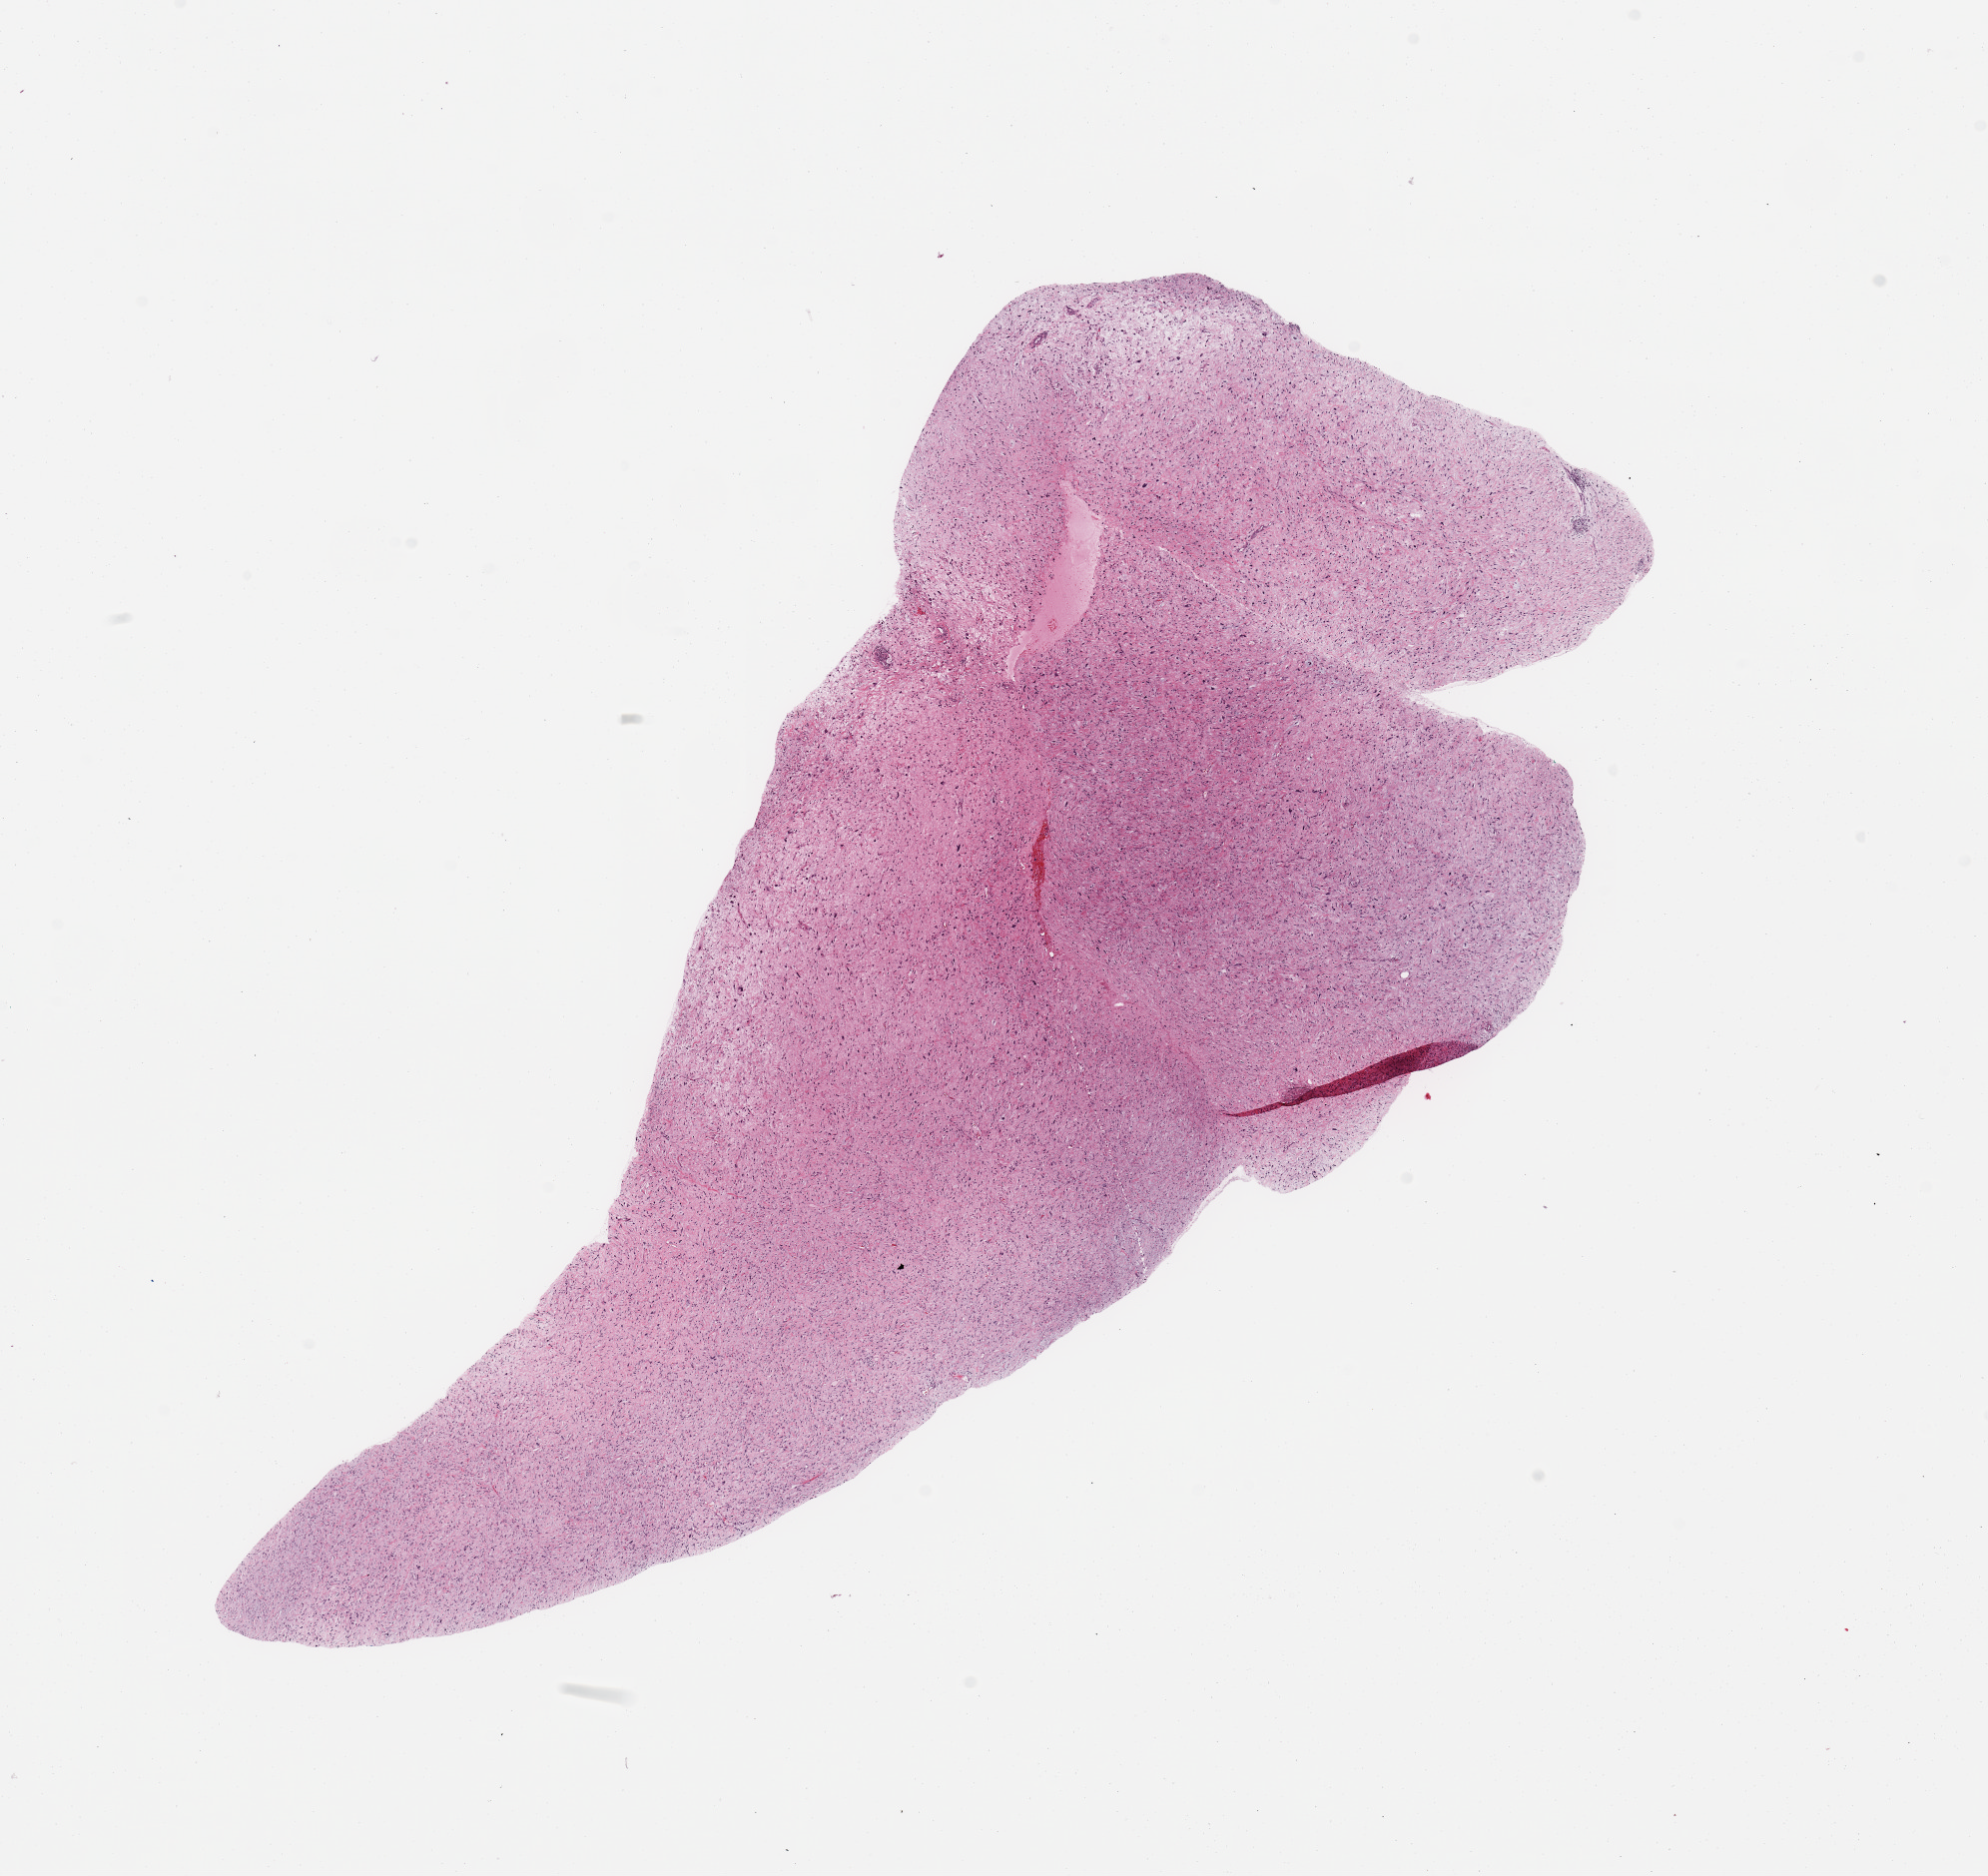
Digitized Hematoxylin and eosin (H&E) stained tissue section (whole slide), whole scanned area (about 15.8 x 14.9 mm, slide scanned at 20x) shown as a low-resolution overview, tumour tissue sample. Patient: female, age 54 years.
Patient diagnosis (cohort enrolment): sarcoma (site not recorded at cohort level).